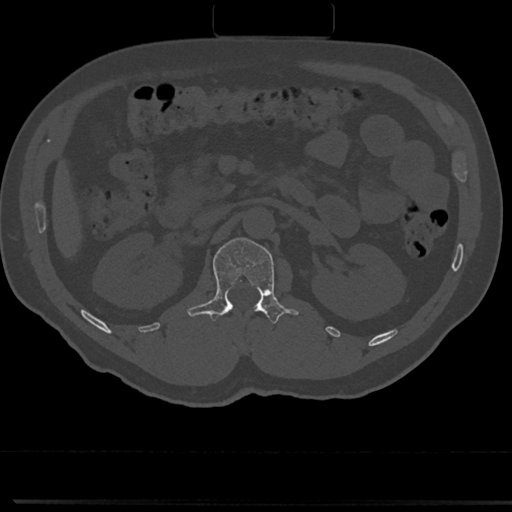
CT including the spine, one axial slice; slice 86 of 817 in the series (ordered by position); bone window (W 1800 / L 400 HU); 0.5 mm slice thickness; 512 × 512 image matrix, field of view 355 × 355 mm. Patient: male, 61 years. From the clinical record (not read from this slice): primary cancer: prostate.
Annotated regions visible in this slice (semi-automatic segmentation, software-assisted and operator-edited):
- L1 vertebra: bounding box (x1, y1, x2, y2) in pixels: (191, 238, 297, 324)